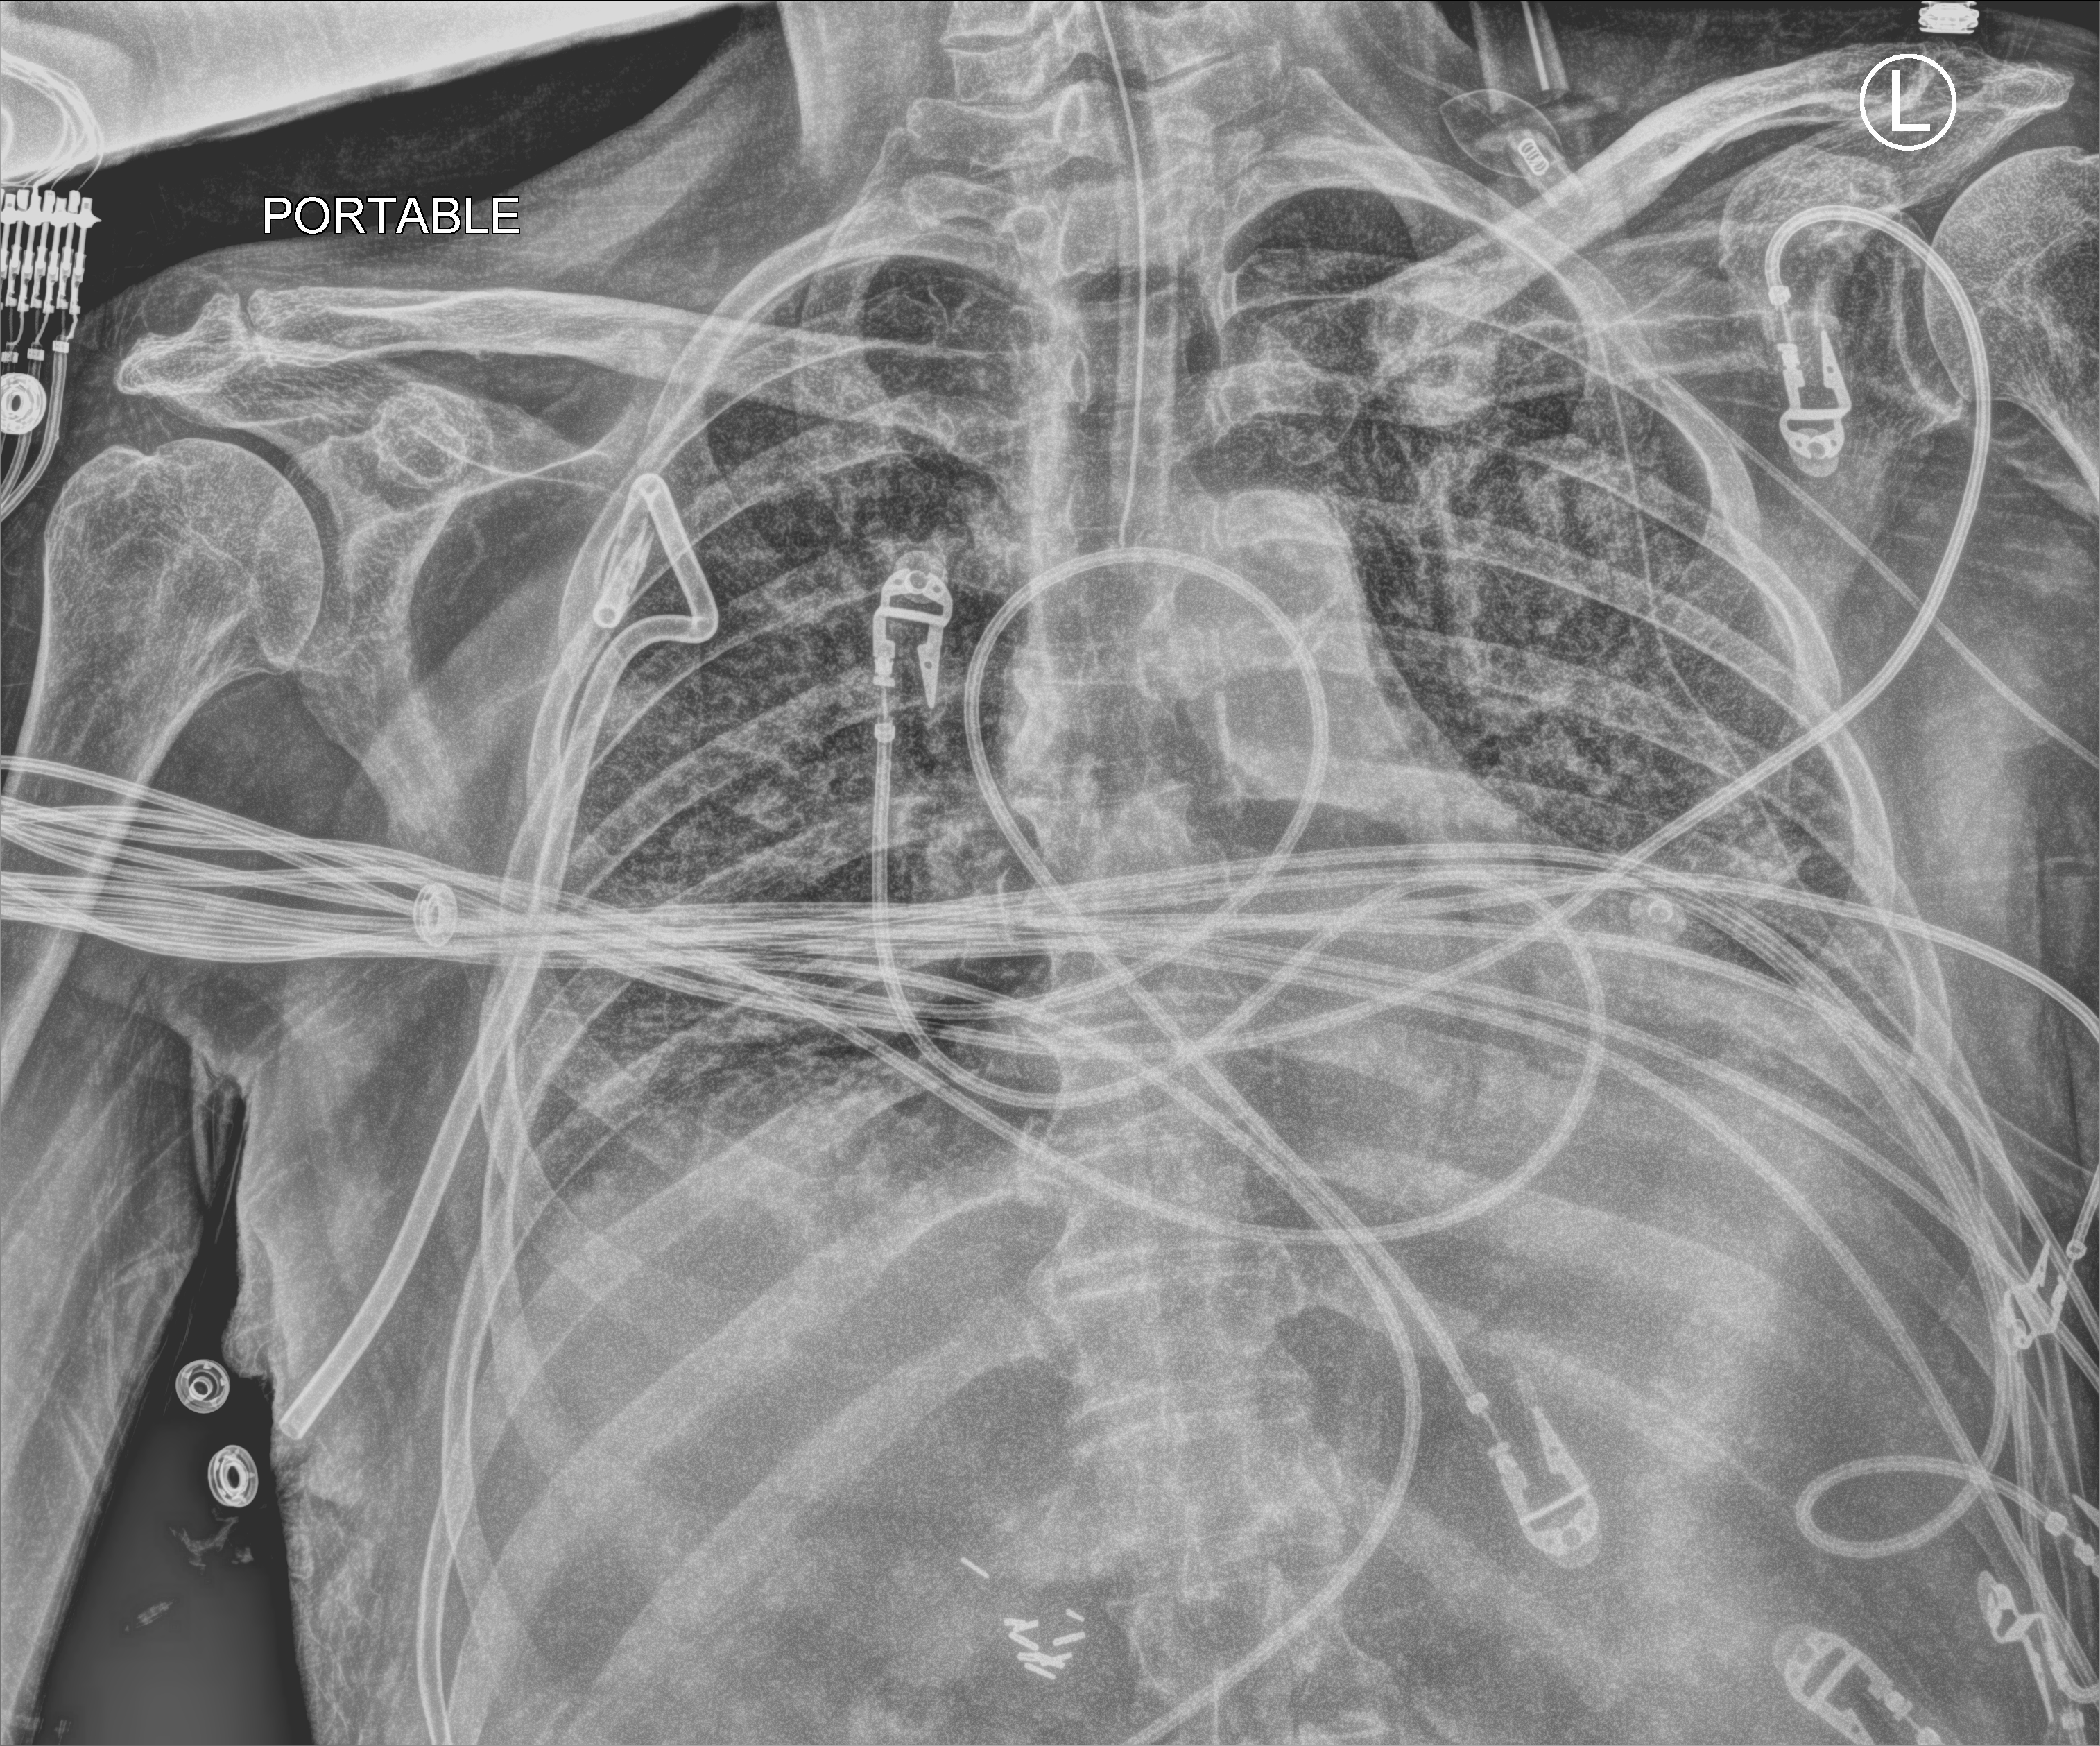
Portable chest radiograph. Male patient hospitalised with COVID-19, age 75–90 years.
From the hospital-stay record, not from the radiograph (when in the stay this image was taken is not recorded): COPD (admission record): no; mechanically ventilated during this hospital stay: yes.